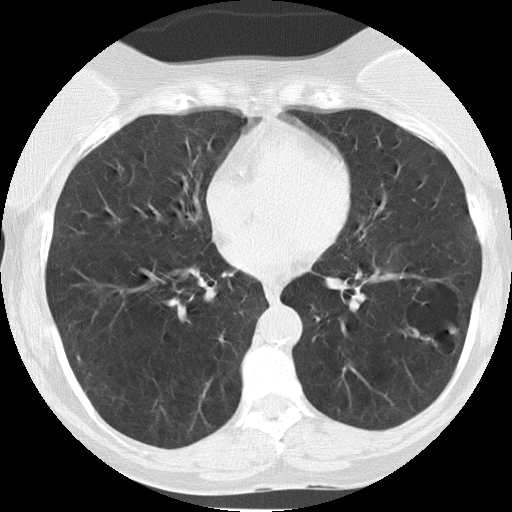
Low-dose screening chest CT, one axial slice. Position 67 of 149 along the scan axis. 120 kVp. Lung window (W 1500 / L -600 HU). 2 mm slice thickness. 512 × 512 image matrix, field of view 290 × 290 mm.
Structures marked on this image (outlined manually by an expert reader):
- lesion 1 (tumor, lower lobe of left lung): bounding box [x1, y1, x2, y2] px = [401, 327, 421, 339]